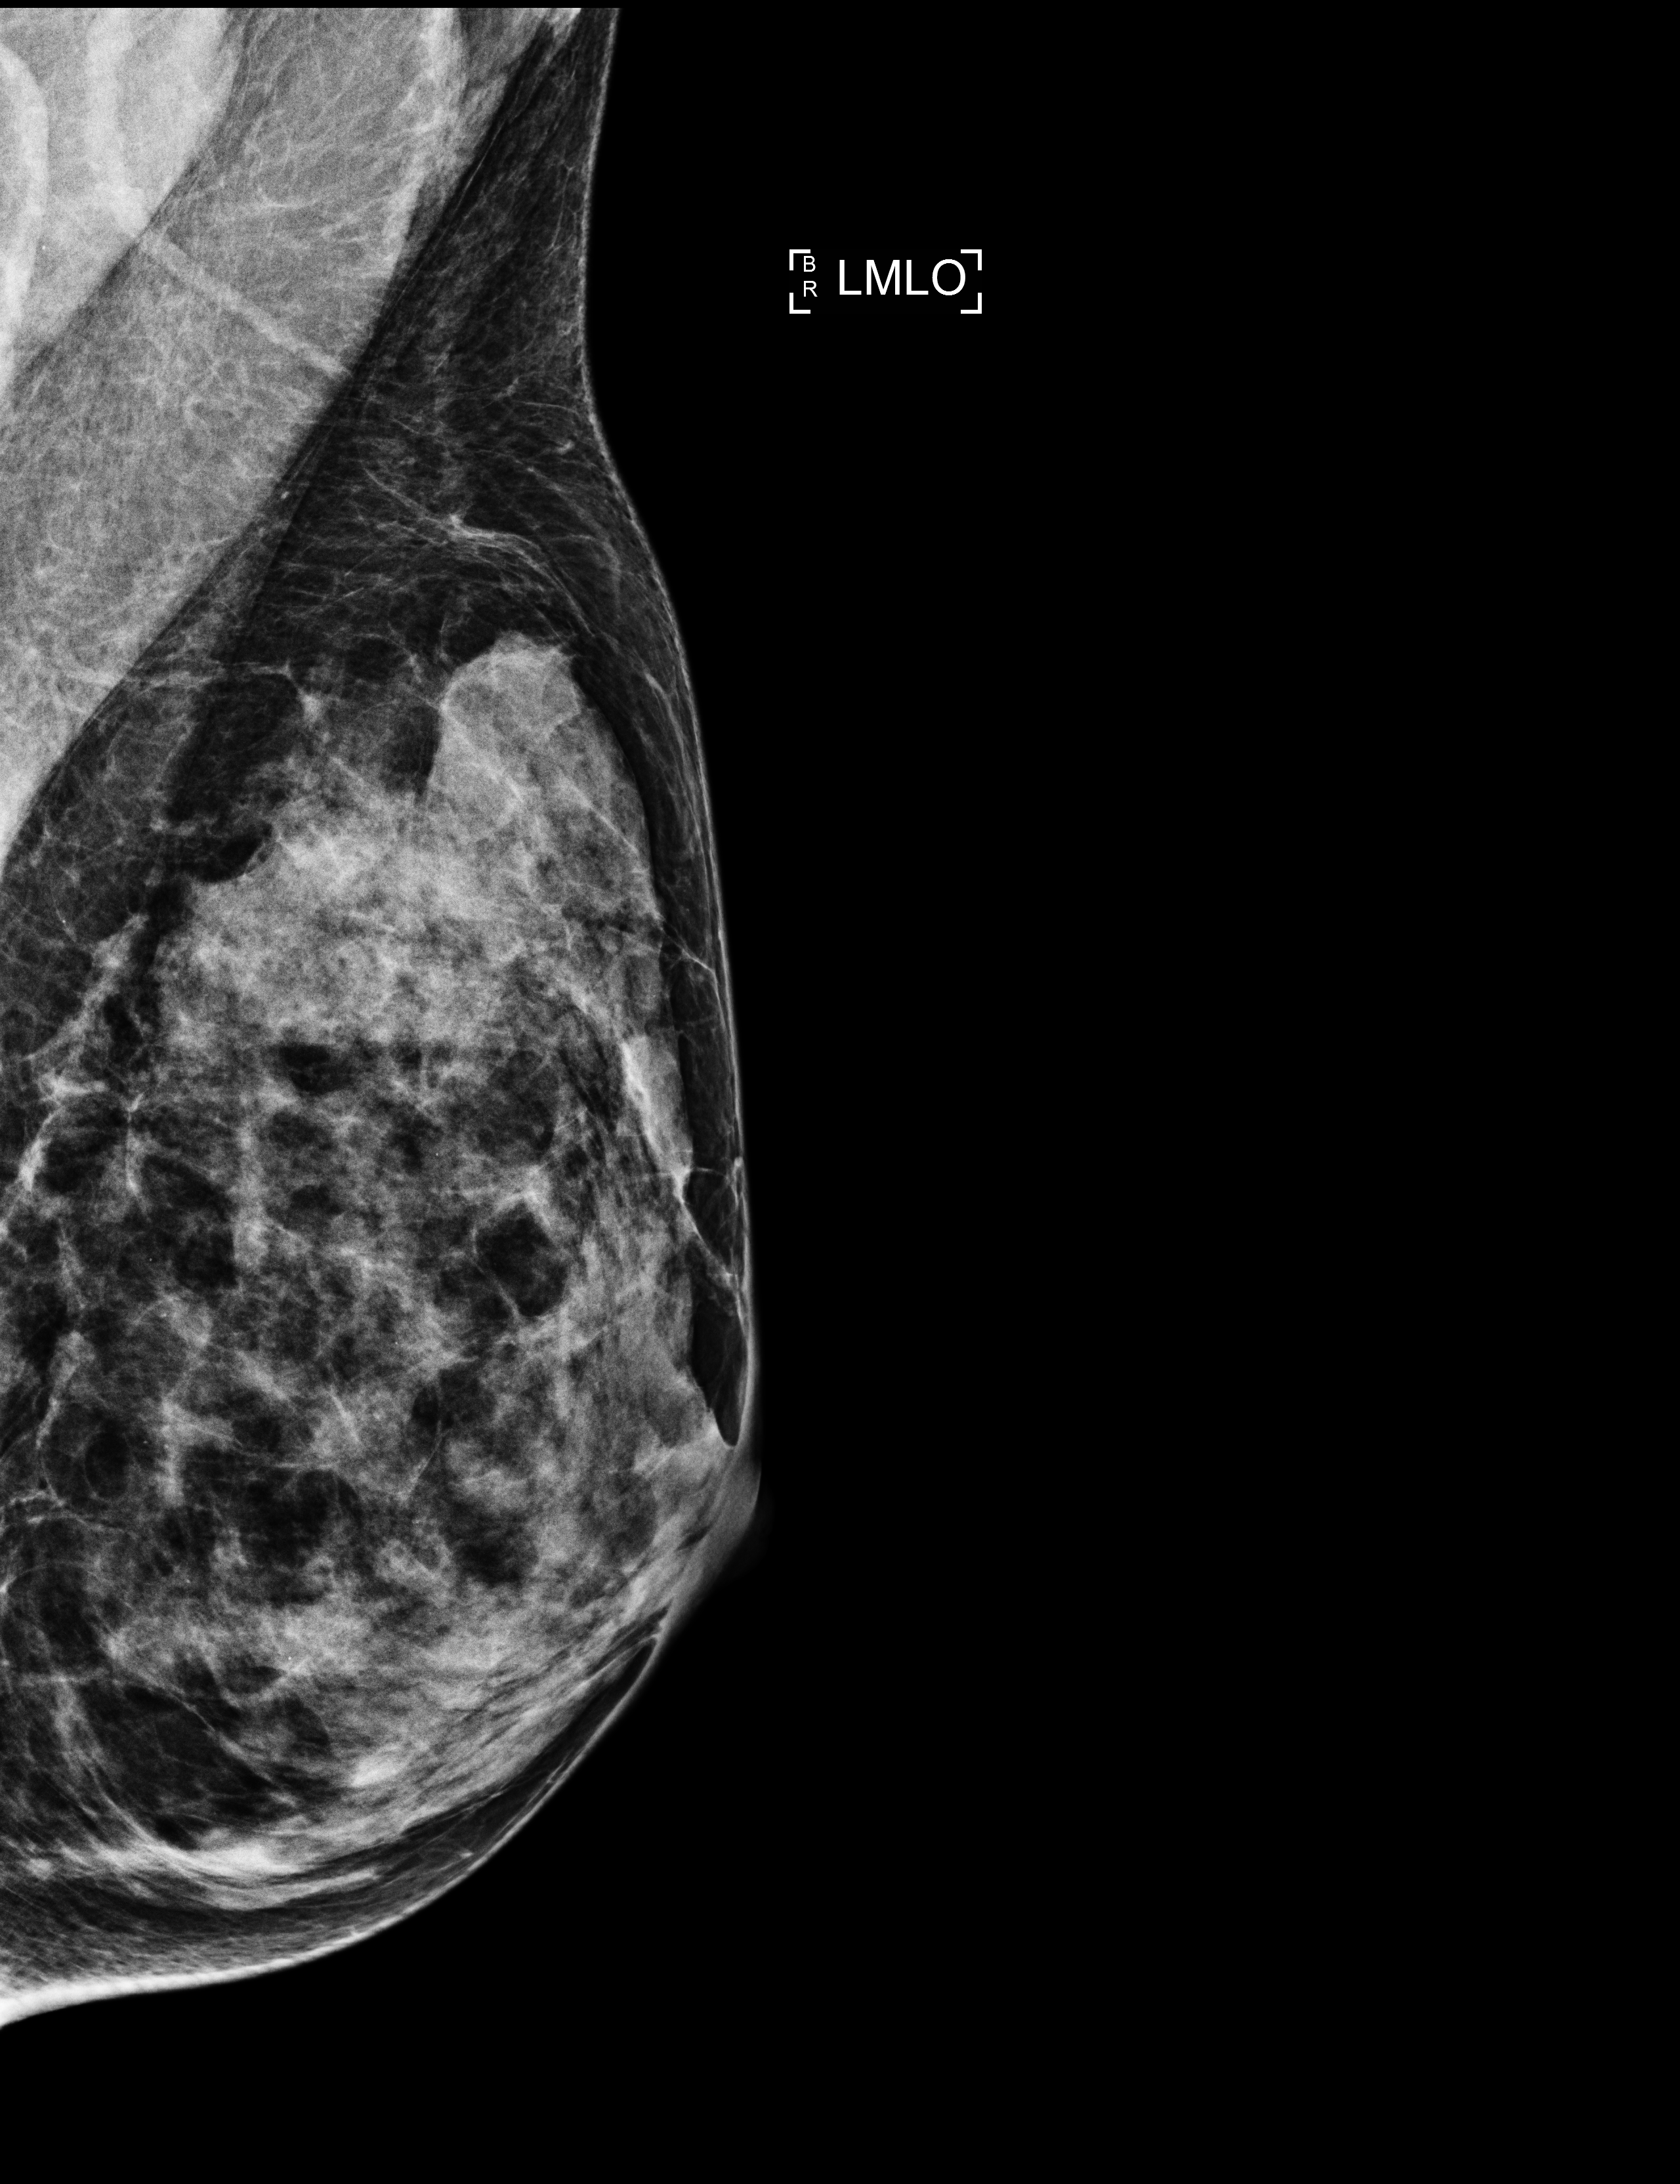
Annual screening mammography examination, system: Selenia Dimensions. Patient aged 47 years (female).
Image type: full-field digital mammogram. Breast: left. Projection: MLO view.